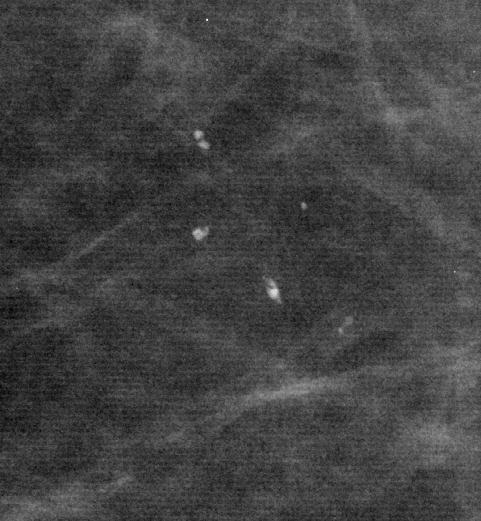
Cropped region of a digitized screen-film mammogram centred on a radiologist-marked abnormality; right breast; CC view; BI-RADS breast density category 1 (scale 1–4).
Calcifications, morphology punctate, distribution clustered; BI-RADS assessment category 4; subtlety rating 5 on a 1 (subtle) to 5 (obvious) scale; pathology (as recorded): benign.